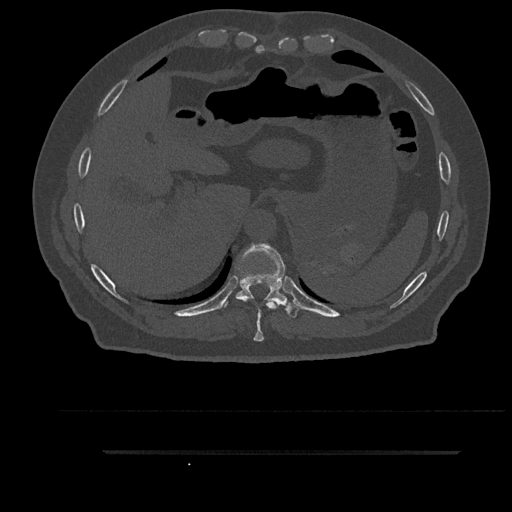
CT including the spine, one axial slice. Position 390 of 797 along the scan axis. 120 kVp. Bone window (W 1800 / L 400 HU). 512 × 512 image matrix, field of view 432 × 432 mm. Patient: male, 63 years. Case-level facts recorded for this patient, not image findings: primary cancer: renal; vertebrae with lytic lesions (as recorded): T8.
Structures marked on this image (semi-automatically segmented with operator editing):
- T10 vertebra: bounding box [x1, y1, x2, y2] px = [223, 243, 301, 318]
- T9 vertebra: [244, 299, 279, 342]